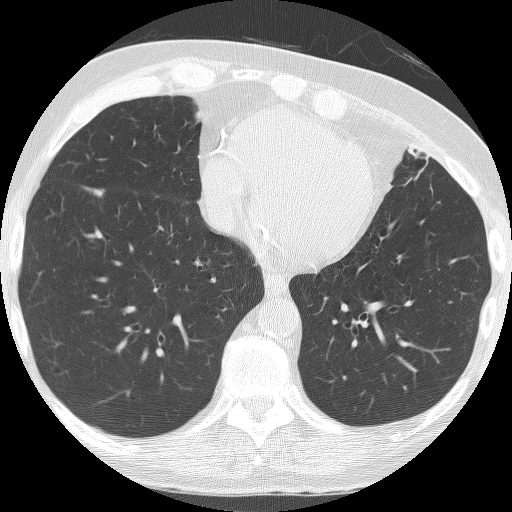
Low-dose screening chest CT, axial slice. First (baseline) screen. Lung window (W 1500 / L -600 HU). 2.5 mm slice thickness. 512 × 512 image matrix. Male, age 74 years at enrolment. Former smoker at enrolment.
Lesion marked by an expert reader, box from (x=74, y=173) to (x=118, y=209) px. The screening reader recorded 4 non-calcified nodules or masses ≥4 mm on this exam (right lower lobe, right lower lobe, right lower lobe, right lower lobe); which of them this box marks is not recorded. Official screen result: positive, change unspecified: nodule(s) >= 4 mm or enlarging nodule(s), mass(es), or other non-specific abnormalities suspicious for lung cancer.